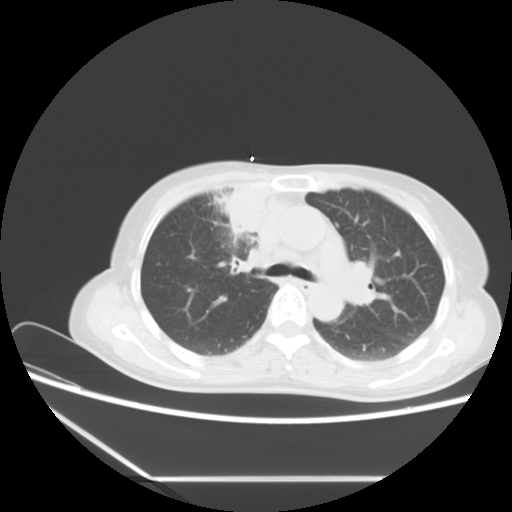
Chest CT, one axial slice; slice 13 of 16 in the series (ordered by position); 120 kVp; lung window (W 1500 / L -600 HU); 512 × 512 image matrix. Patient: female, 63 years. From the clinical record (not read from this slice): clinical TNM (as recorded): T2b N1 M0.
Structures marked on this image (bounding box drawn by a radiologist):
- lung tumour (recorded histology: adenocarcinoma): bounding box <212,176,272,242> (left, top, right, bottom; pixels)